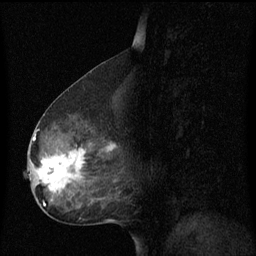
Breast MRI (dynamic contrast-enhanced), one sagittal slice; position 34 of 60 along the scan axis; dynamic contrast-enhanced series, image 2 of 3 at this slice position (ordered by acquisition); 1.5 T; TE 4.2 ms, TR 8.4 ms; 256 × 256 image matrix, field of view 200 × 200 mm. Patient: female, 49 years. Case-level facts recorded for this patient, not image findings: setting: breast cancer imaged before/during neoadjuvant chemotherapy; receptor status: HR-positive, HER2-negative.
Outlined on this slice (semi-automatically segmented with operator editing):
- analysis volume of interest (the breast-tissue region the enhancement analysis was run in; not a lesion): bounding box <28,126,121,201> (left, top, right, bottom; pixels)
- tumour enhancement mask (voxels above the 70 % enhancement threshold inside the analysis volume of interest): <34,136,114,193>